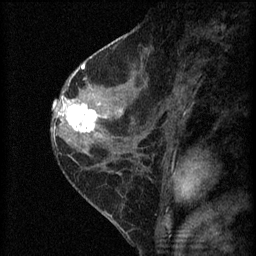
Breast MRI (dynamic contrast-enhanced), one sagittal slice; slice 30 of 60 in the series (ordered by position); 3 images stored at this slice position (order not interpretable as contrast timing); 1.5 T; TE 4.2 ms, TR 8.2 ms; 2 mm slice thickness; 256 × 256 image matrix. Female patient, age 45 years.
Annotated regions visible in this slice (semi-automatic segmentation, software-assisted and operator-edited):
- analysis volume of interest (the breast-tissue region the enhancement analysis was run in; not a lesion): bounding box (x1, y1, x2, y2) in pixels: (62, 98, 104, 139)
- tumour enhancement mask (voxels above the 70 % enhancement threshold inside the analysis volume of interest): (62, 100, 100, 133)